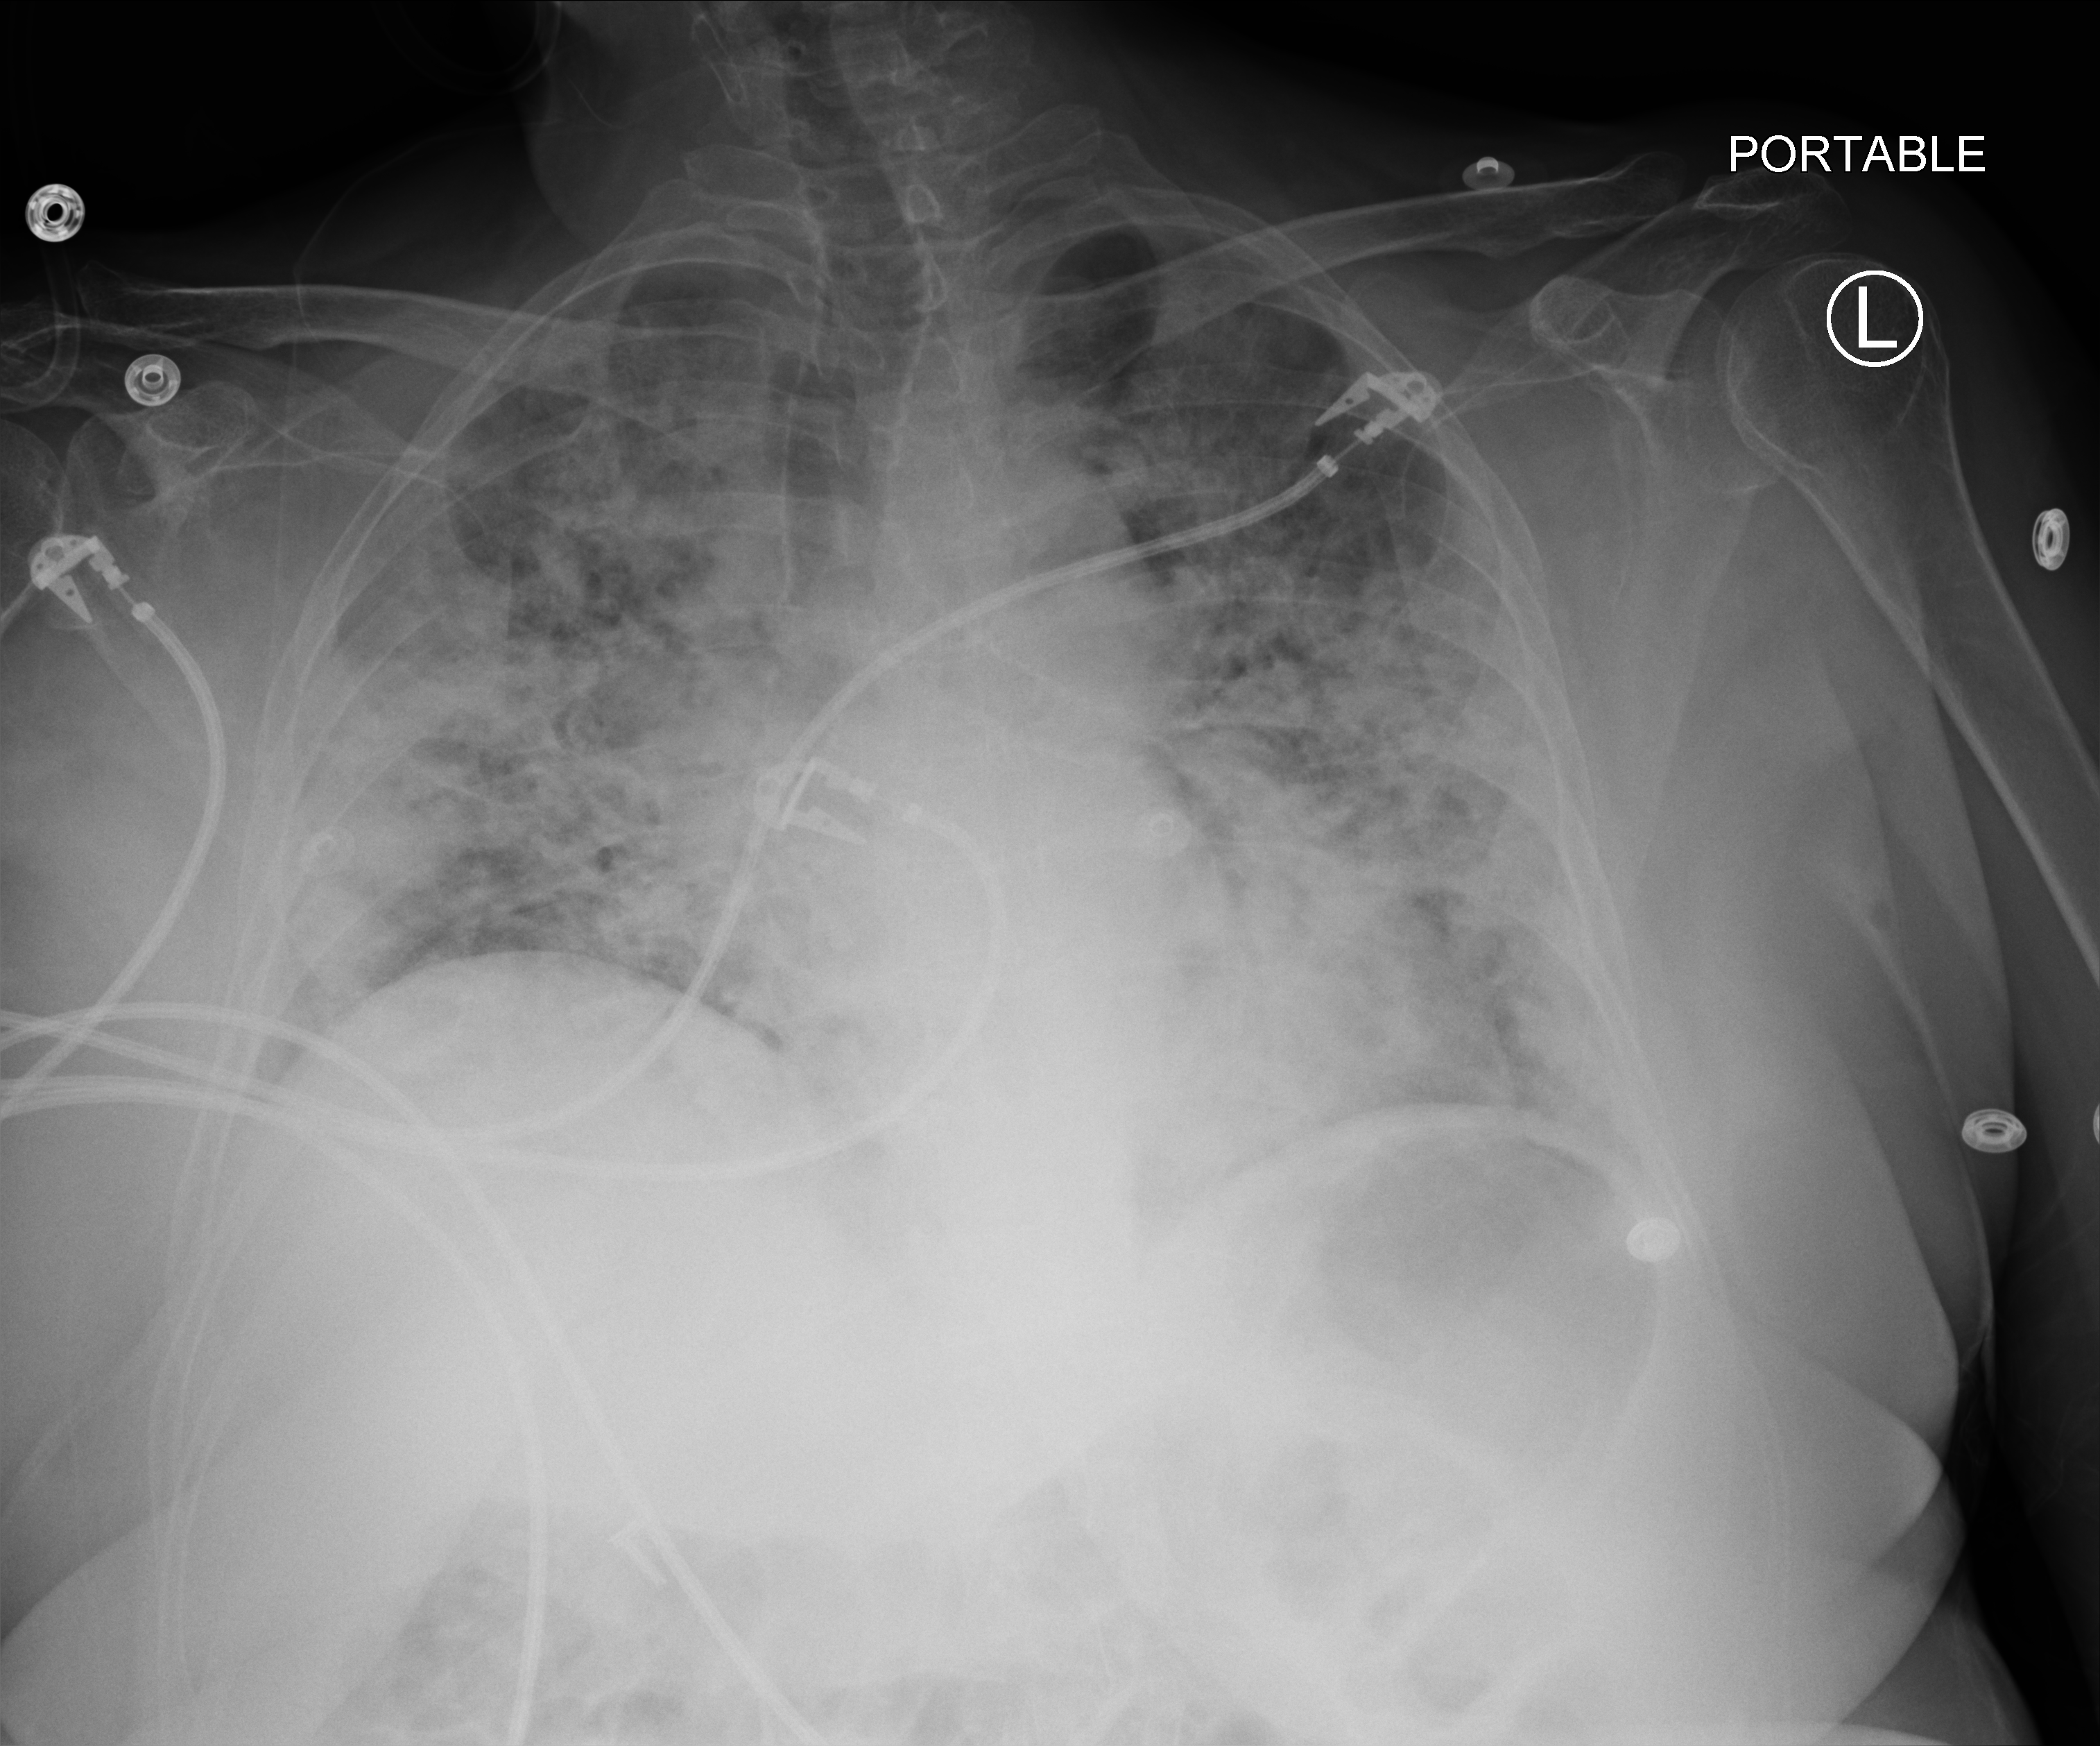
Bedside chest radiograph (computed radiography), anteroposterior (AP) projection. Patient hospitalised with COVID-19; female, aged 18–59 years.
From the hospital-stay record, not from the radiograph (when in the stay this image was taken is not recorded):
- mechanically ventilated during this hospital stay: yes